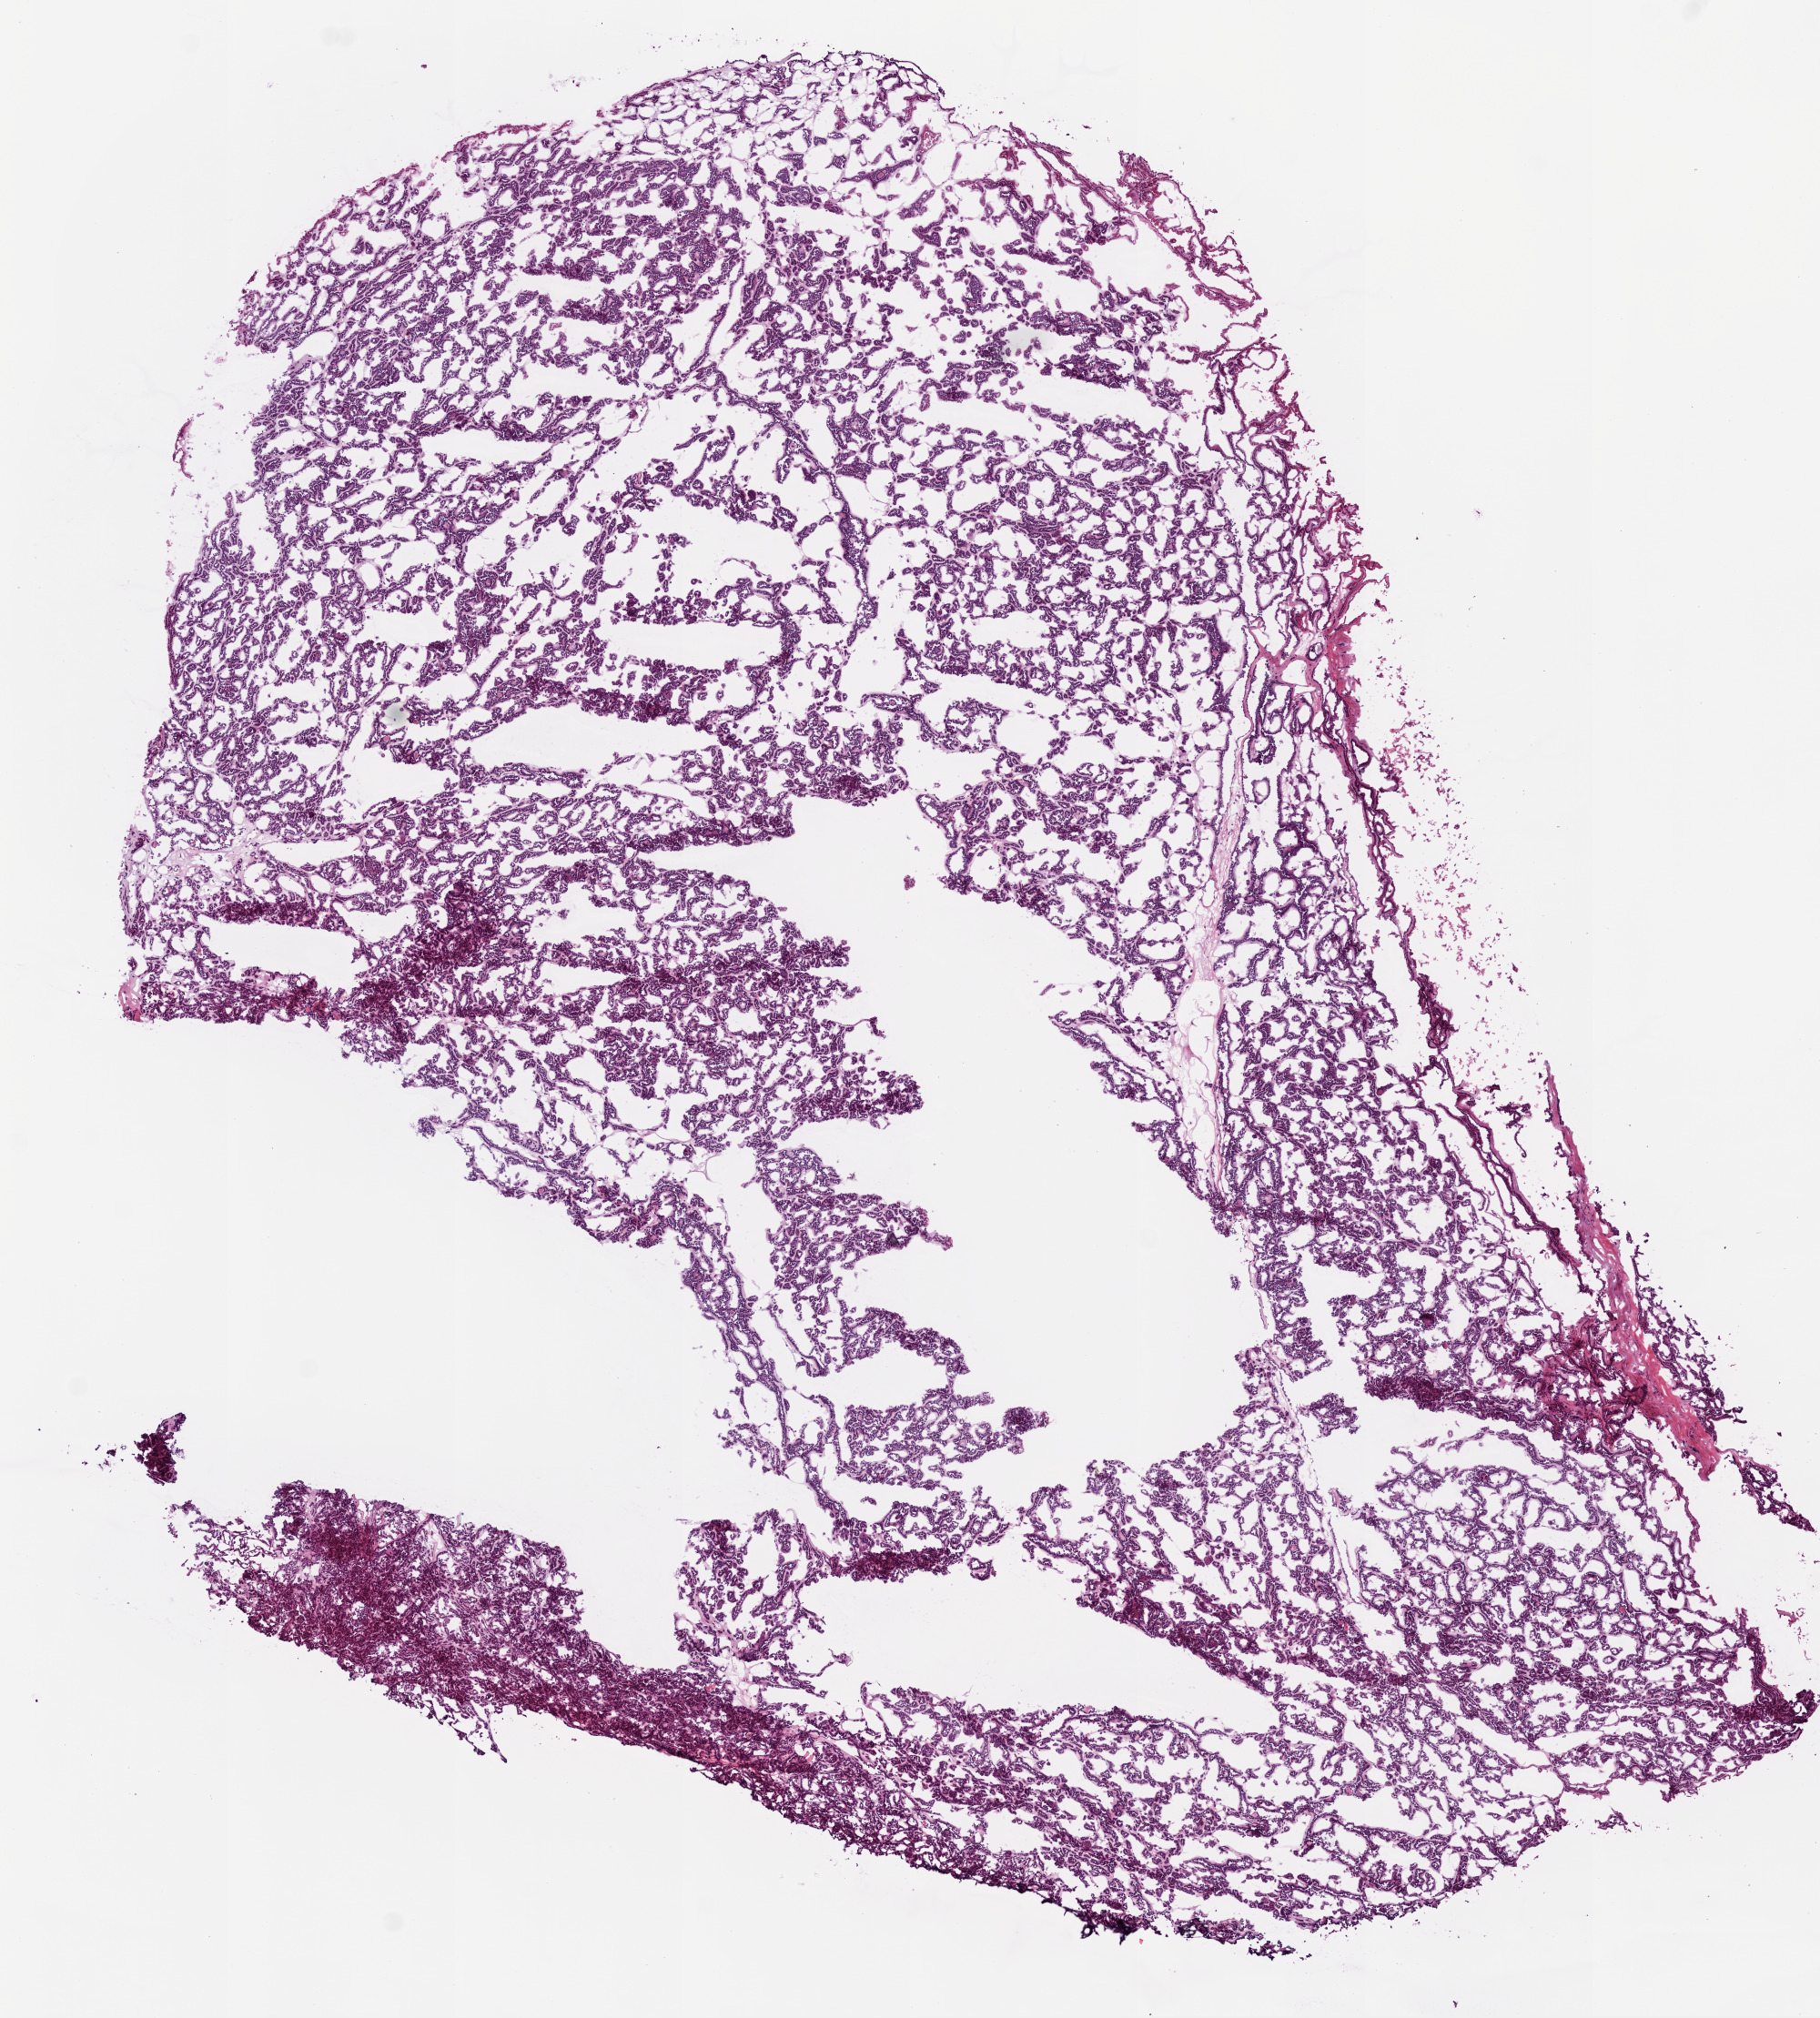
Whole-slide histology image, H&E, a low-resolution overview of the entire scanned area, about 8.0 x 8.9 mm (slide scanned at 20x); frozen section; primary tumour sample from the kidney. Female patient; age at initial diagnosis 54 years. Pathologist review of this section (percent, as recorded): tumour cells 92%, tumour nuclei 80%, normal cells 0%, stromal cells 5%, necrosis 3%.
• diagnosis: Papillary adenocarcinoma, NOS